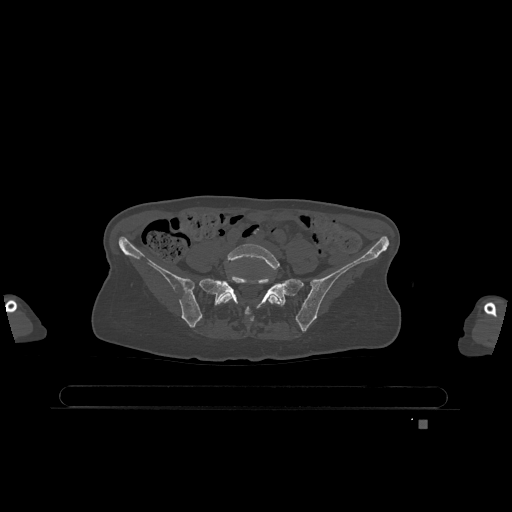
CT including the spine, one axial slice. Position 213 of 1317 along the scan axis. Bone window (W 1800 / L 400 HU). 0.5 mm slice thickness. 512 × 512 image matrix. Female patient, age 74 years. Case-level facts recorded for this patient, not image findings: primary cancer: lung; vertebrae with lytic lesions (as recorded): T1, T4, T5, T6, L4, L5.
Outlined on this slice (semi-automatic segmentation, software-assisted and operator-edited):
- L5 vertebra: bounding box (x1, y1, x2, y2) in pixels: (217, 244, 282, 315)